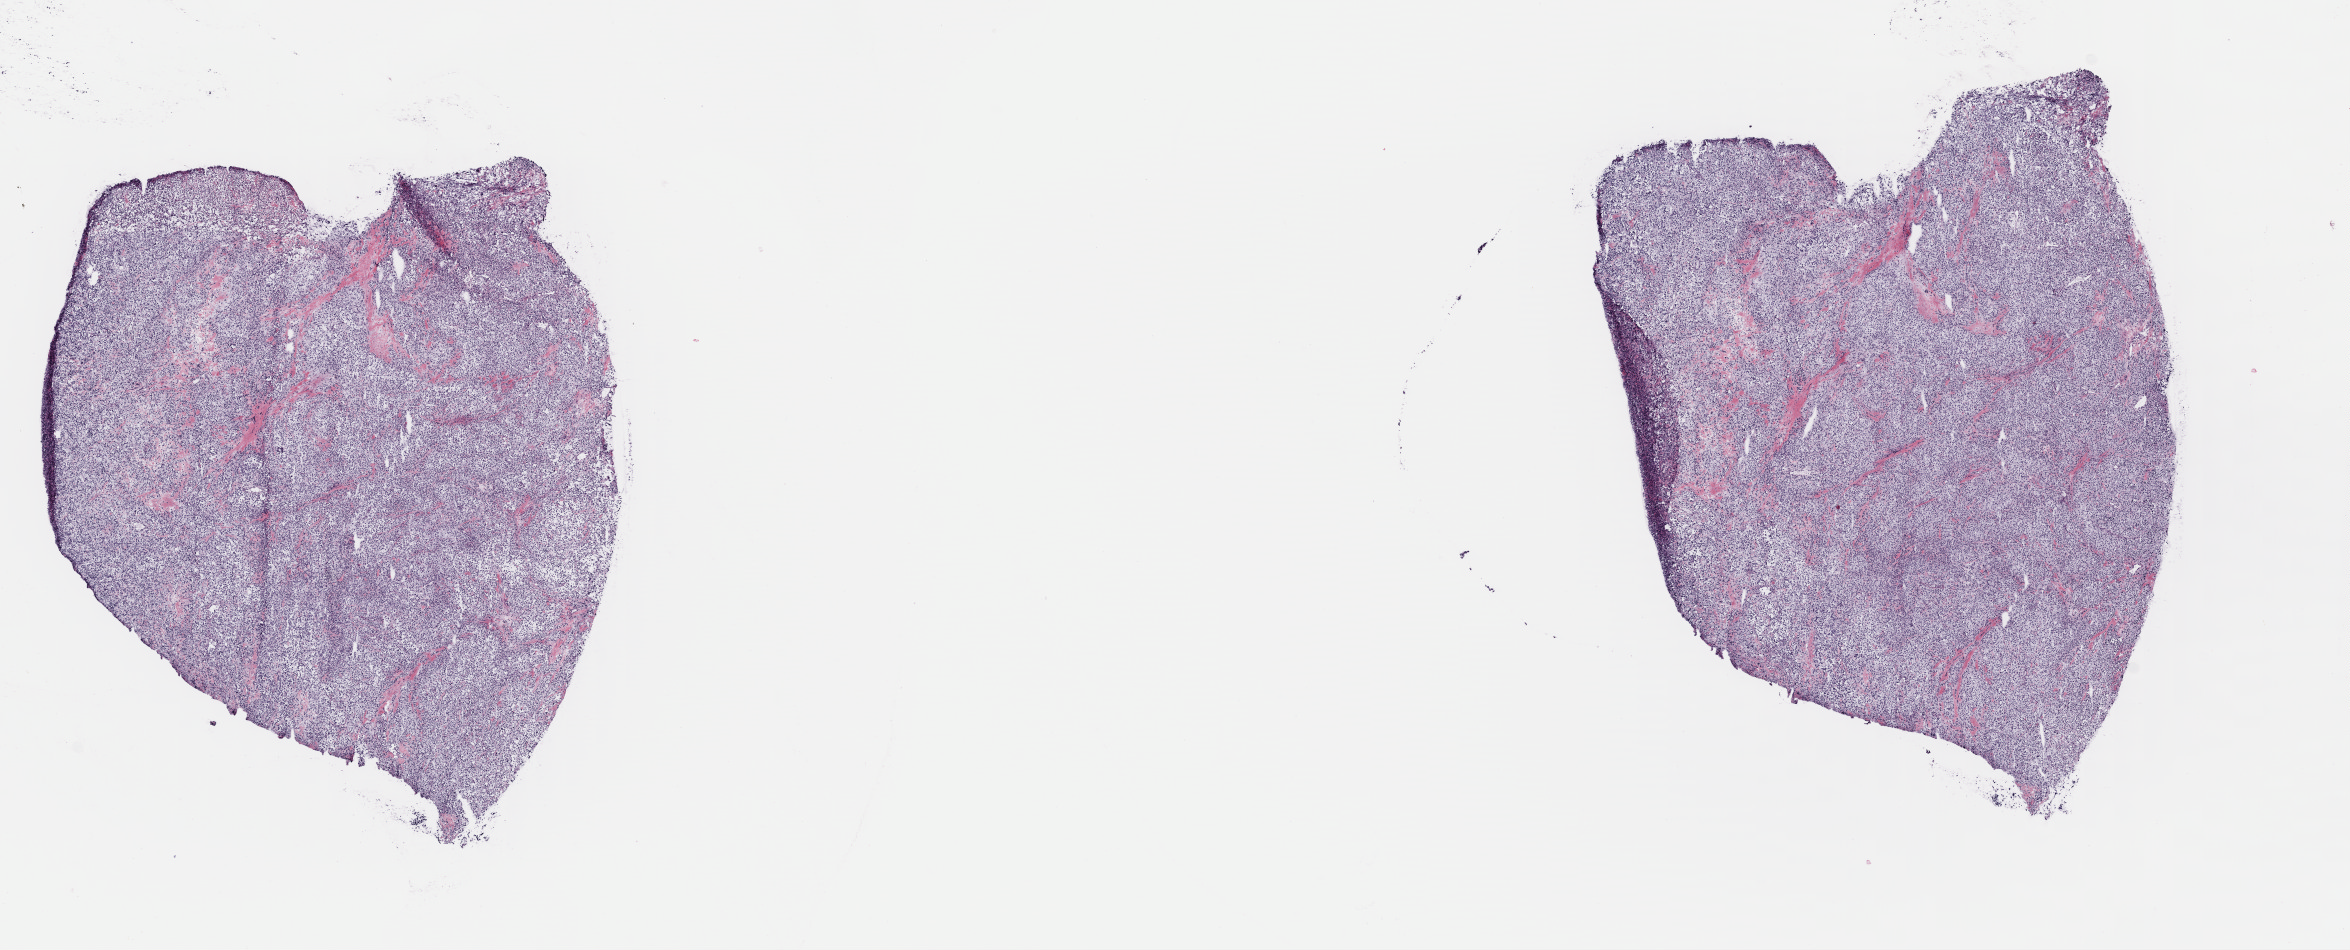
Digitized H&E tissue section (whole slide) — low-resolution overview of the scanned area, about 18.5 x 7.5 mm. Frozen section. Primary tumour sample from the adrenal gland. Female, age 42 years at initial diagnosis. Composition of this section per pathologist review: tumour cells 90%, tumour nuclei 100%, normal cells 0%, stromal cells 10%, necrosis 0%. Infiltration values recorded for this section: lymphocyte infiltration 0%, monocyte infiltration 0%, neutrophil infiltration 0%.
• diagnosis: Pheochromocytoma, malignant
• laterality: left
• lymph nodes positive (case pathology): 13 of 15 examined